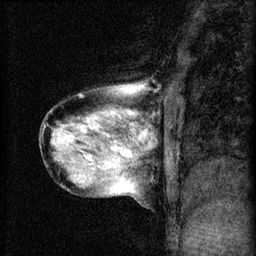
Breast MRI (dynamic contrast-enhanced), one sagittal slice; slice 23 of 60 in the series (ordered by position); 3 images stored at this slice position (order not interpretable as contrast timing); 1.5 T; TE 4.2 ms, TR 8.2 ms; 2 mm slice thickness; 256 × 256 image matrix, field of view 180 × 180 mm. Patient: female, 40 years.
Outlined on this slice (semi-automatic segmentation, software-assisted and operator-edited):
- analysis volume of interest (the breast-tissue region the enhancement analysis was run in; not a lesion): box from (x=39, y=80) to (x=164, y=197) px
- tumour enhancement mask (voxels above the 70 % enhancement threshold inside the analysis volume of interest): (x=61, y=112)–(x=148, y=167)